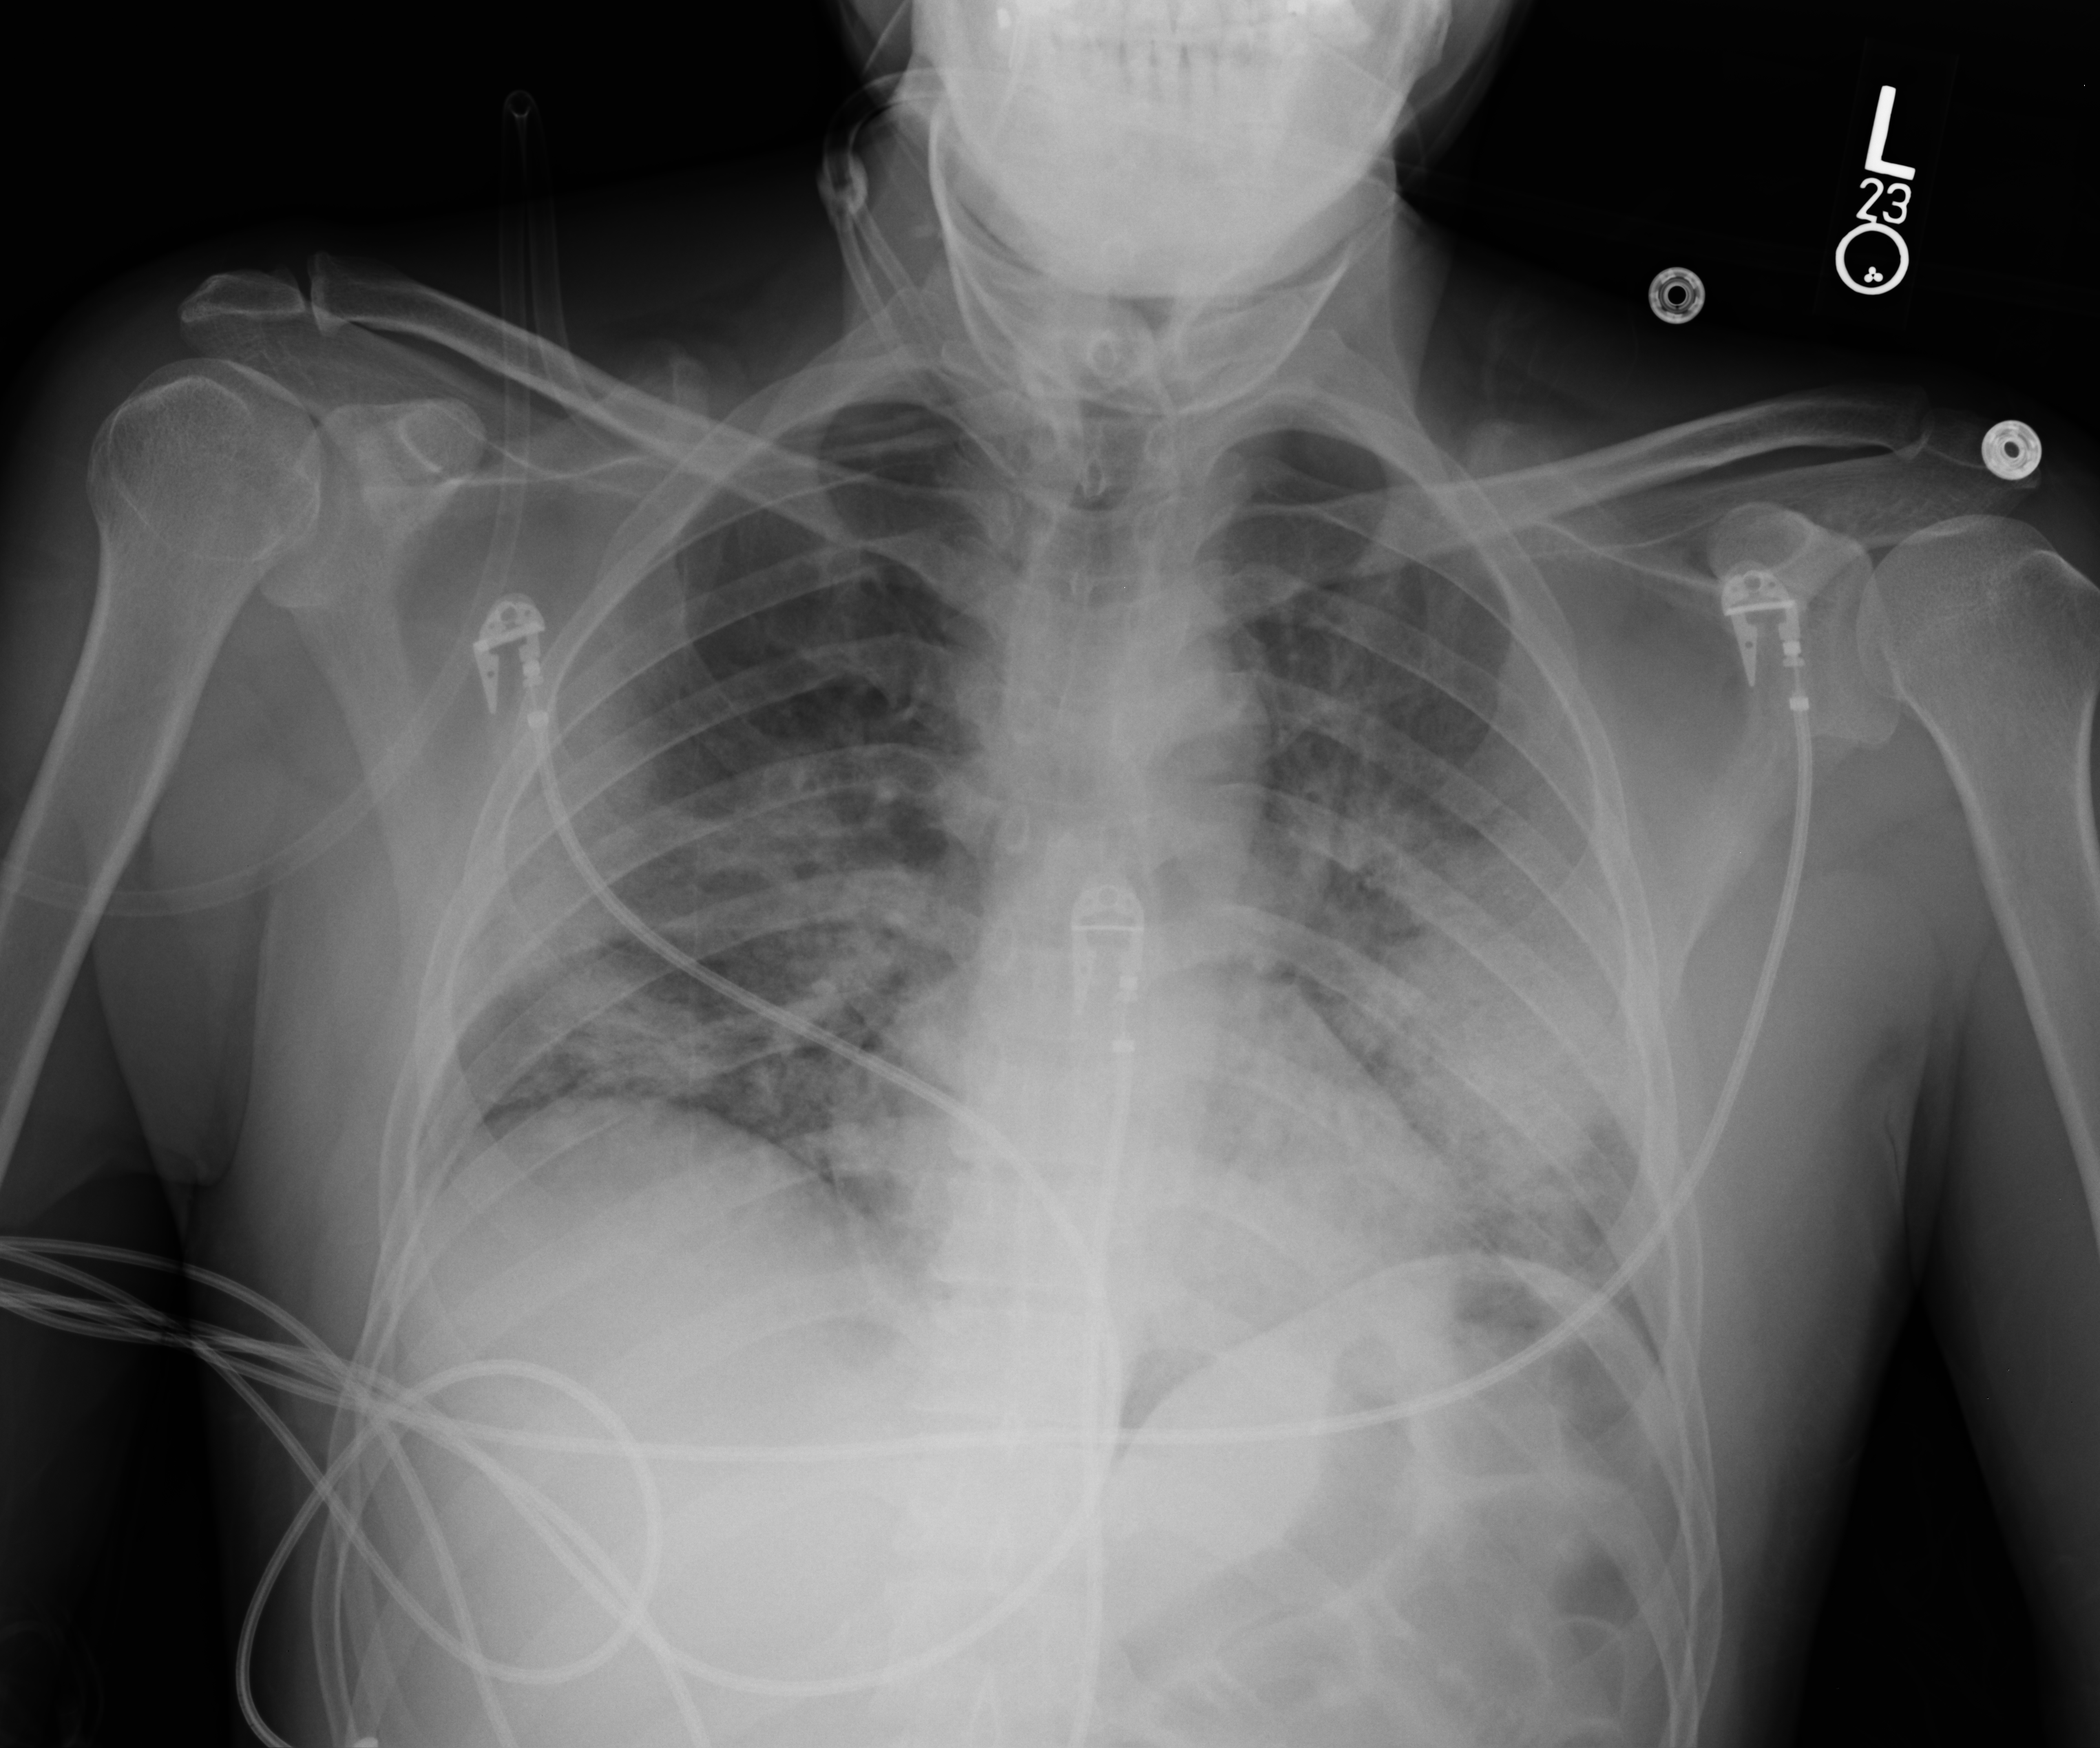
Chest X-ray (portable), anteroposterior (AP) projection. Patient hospitalised with COVID-19; male, aged 18–59 years.
Hospital-stay facts (about this admission, not read from this image; timing relative to this image not recorded): length of hospital stay: 14 days.